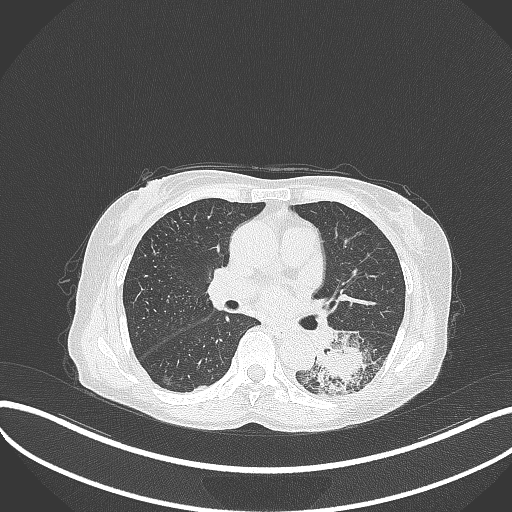
Chest CT, one axial slice. Position 171 of 370 along the scan axis. Reconstruction kernel B70f. Lung window (W 1500 / L -600 HU). 1 mm slice thickness. 512 × 512 image matrix, field of view 400 × 400 mm. Female patient, age 78 years. From the clinical record (not read from this slice): clinical TNM (as recorded): T3 N0 M1.
Outlined on this slice (rectangle marked by the reading radiologist):
- lung tumour (recorded histology: squamous cell carcinoma): box from (x=315, y=328) to (x=382, y=397) px